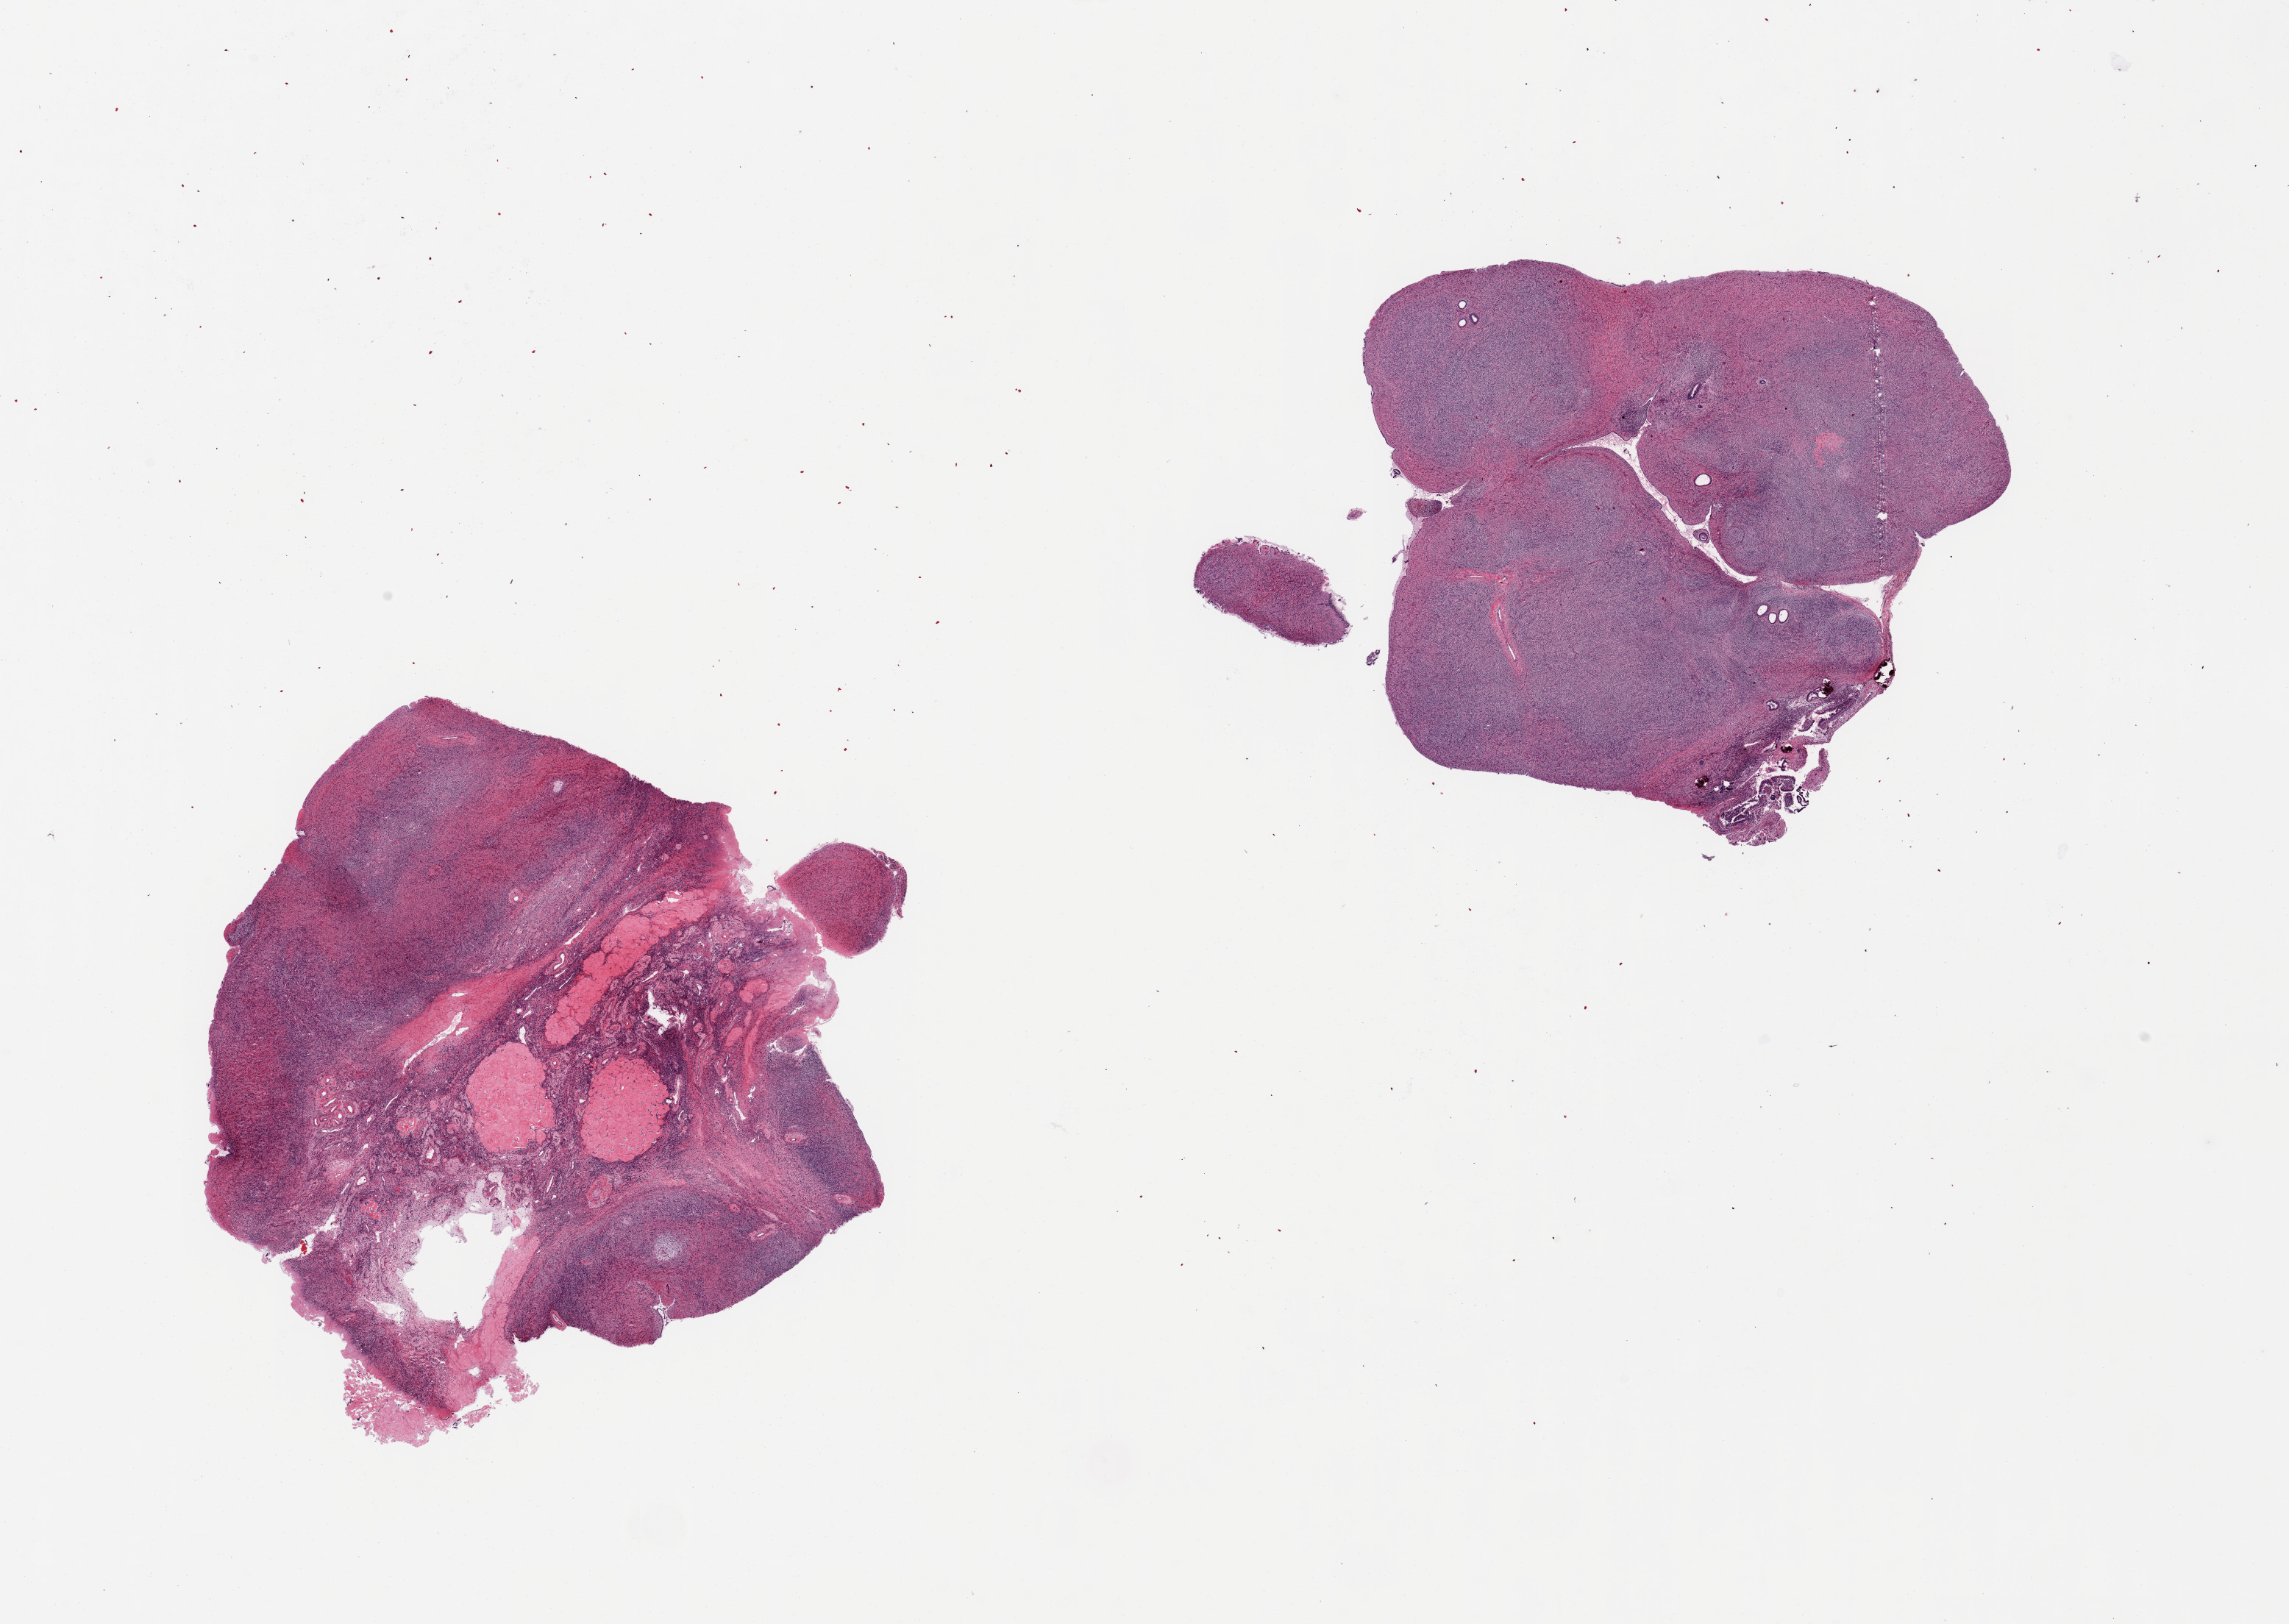
Haematoxylin and eosin whole-slide image, brightfield, whole scanned area (about 24.6 x 17.5 mm, from a 20x scan) shown as a low-resolution overview, PAXgene-fixed paraffin-embedded (PFPE) section, section of ovary (target tissue), tissue donor sample. Donor: female.
• pathologist's review note for this sample: 2 ~7 x 6 mm post-menopausal stroma